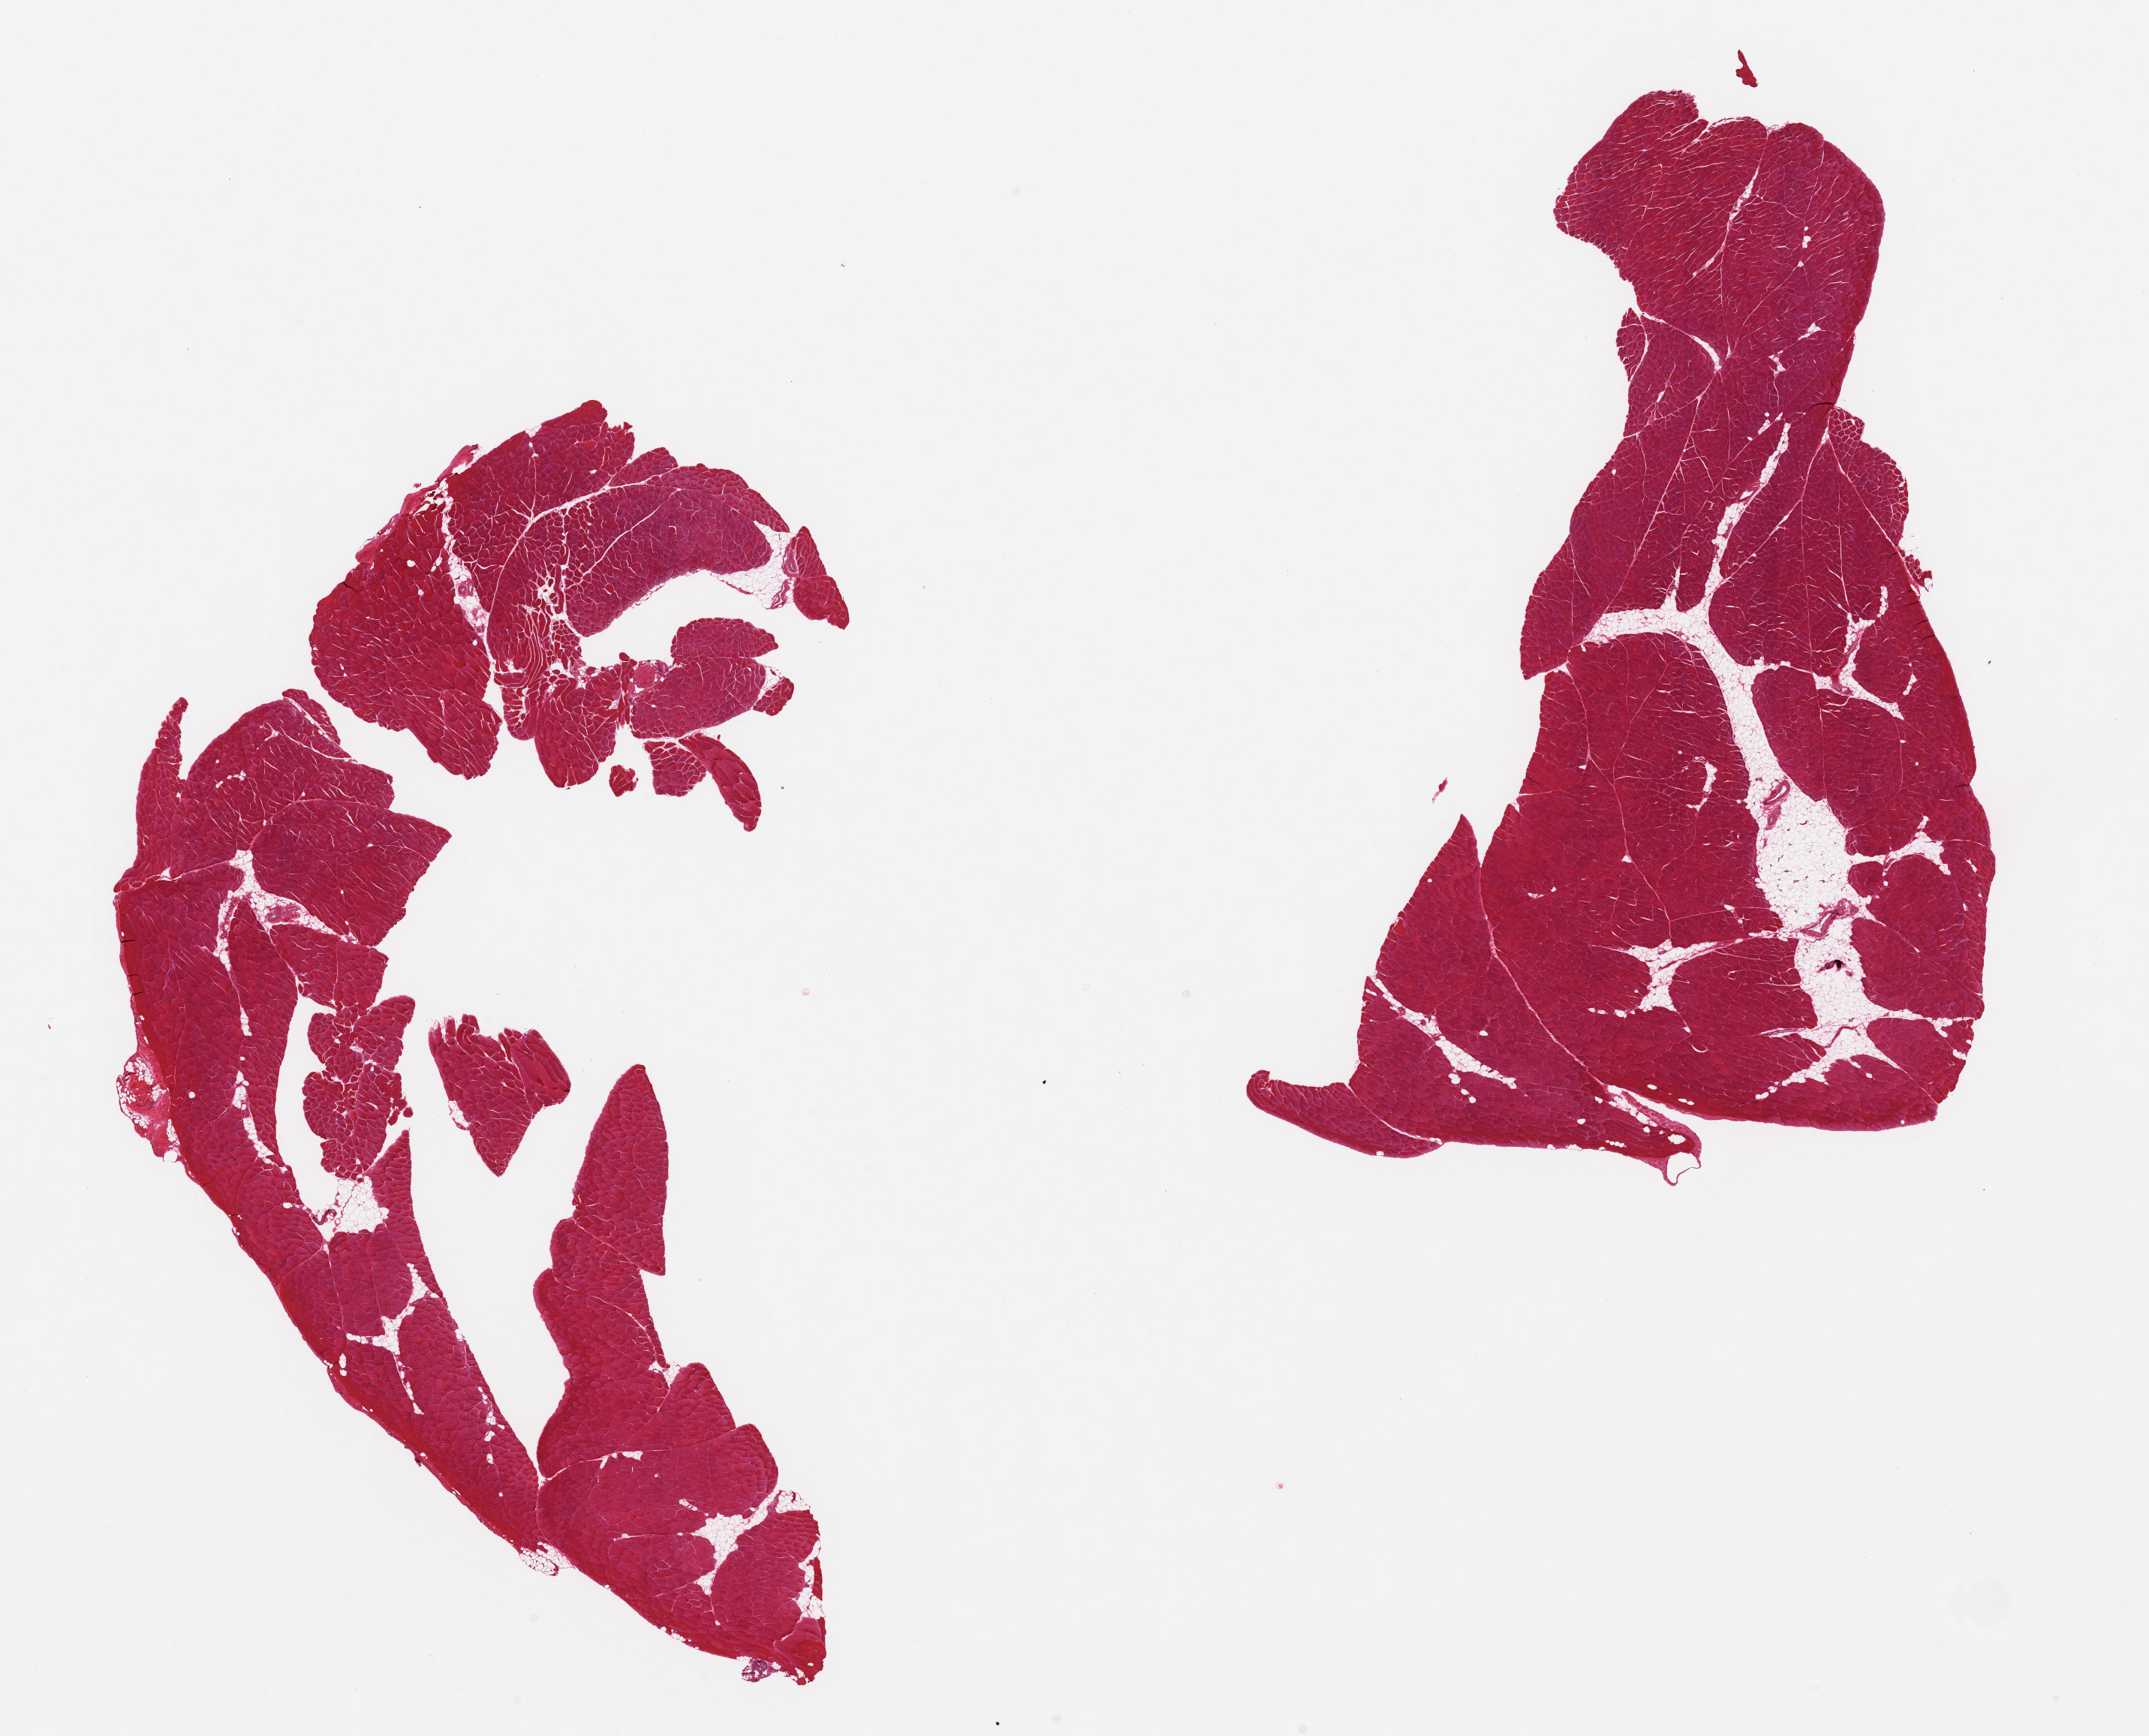
Whole-slide image, haematoxylin and eosin stain, low-resolution overview of the scanned area, about 22.6 x 18.3 mm (slide scanned at 20x), PAXgene-fixed paraffin-embedded (PFPE) section, section of skeletal muscle (target tissue), tissue donor sample.
Pathologist's review note for this sample: 2 pieces, ~10-15% interstitial fat/vascular elements.